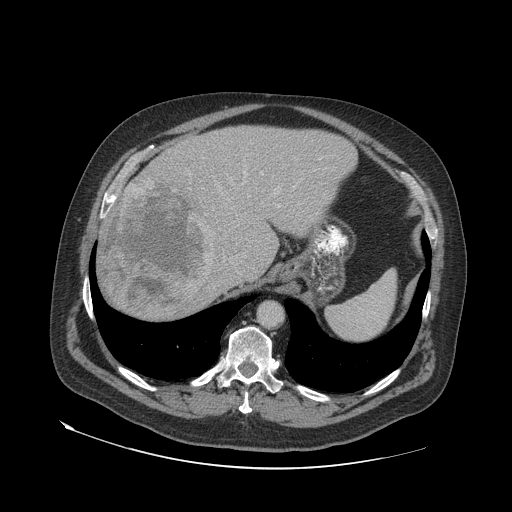
Contrast-enhanced abdominal CT (liver protocol), one axial slice. Position 54 of 79 along the scan axis. Soft-tissue window (W 400 / L 40 HU). 2.5 mm slice thickness. 512 × 512 image matrix. From the clinical record (not read from this slice): diagnosis: hepatocellular carcinoma (patient treated with transarterial chemoembolisation; whether this scan precedes or follows treatment is not stated here); TNM stage (as recorded): Stage-IVA; Child-Pugh class: A; tumour differentiation: well differentiated; tumour nodularity: multinodular.
Structures marked on this image (semi-automatic segmentation, software-assisted and operator-edited):
- abdominal aorta: bounding box <260,303,283,327> (left, top, right, bottom; pixels)
- liver parenchyma outside the tumour (the mass and vessels are separate outlines, so this box may not span the whole liver): <100,126,356,320>
- mass: <103,179,216,319>
- liver vessels: <244,172,280,207>